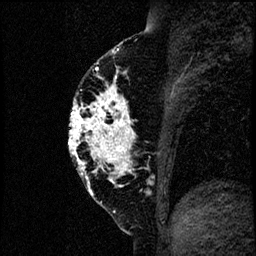
Breast MRI (dynamic contrast-enhanced), one sagittal slice. Slice 35 of 60 in the series (ordered by position). Dynamic contrast-enhanced study with each time point stored as its own series, time point 2 of 4 at this slice position (early post-contrast, ordered by acquisition time). 1.5 T. TE 4.2 ms, TR 17.6 ms. 256 × 256 image matrix, field of view 200 × 200 mm. Patient: female, 40 years. Case-level facts recorded for this patient, not image findings: setting: breast cancer imaged before/during neoadjuvant chemotherapy; receptor status: HER2-positive.
Outlined on this slice (semi-automatic segmentation, software-assisted and operator-edited):
- analysis volume of interest (the breast-tissue region the enhancement analysis was run in; not a lesion): bounding box <66,55,185,206> (left, top, right, bottom; pixels)
- tumour enhancement mask (voxels above the 100 % enhancement threshold inside the analysis volume of interest): <68,63,131,181>